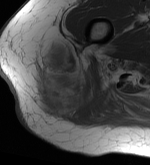
MRI of an extremity soft-tissue mass, one axial slice; position 15 of 56 along the scan axis; MR volume resampled by the dataset authors to the PET/CT grid (not the native acquisition matrix); 150 × 165 image matrix. Female patient. From the clinical record (not read from this slice): histological type: epithelioid sarcoma with vascular differentiation; site of the primary tumour: right buttock.
Annotated regions visible in this slice (expert contour drawn on MRI and transferred to this co-registered scan by the dataset authors):
- gross tumour volume (mass): bounding box <34,45,95,119> (left, top, right, bottom; pixels)